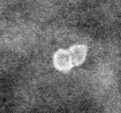
Cropped region of a digitized screen-film mammogram centred on a radiologist-marked abnormality; left breast; CC view.
Calcifications, morphology round and regular / lucent centered; BI-RADS assessment category 2; benign; no additional work-up was recommended (benign without callback).